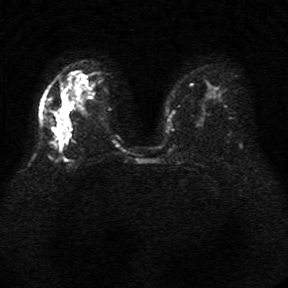
Breast MRI, one axial slice. Position 21 of 34 along the scan axis. Diffusion-weighted series; image 2 of 4 stored at this slice position (different b-values; order by instance number). 1.5 T. 5 mm slice thickness. 288 × 288 image matrix, field of view 340 × 340 mm. Female patient.
Annotated regions visible in this slice (outlined manually by an expert reader):
- tumour on diffusion-weighted imaging: bounding box (x1, y1, x2, y2) in pixels: (46, 113, 68, 141)